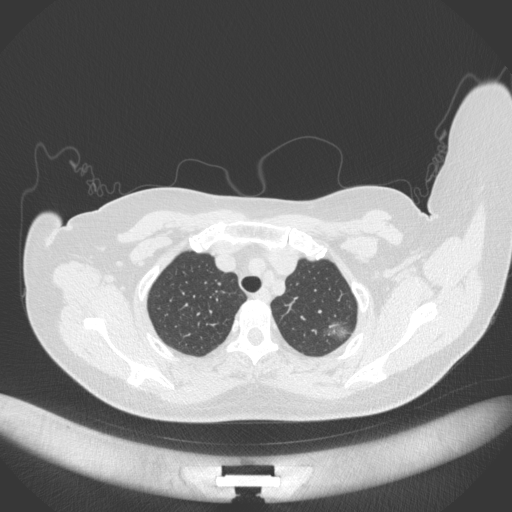
Chest CT, one axial slice. Position 311 of 386 along the scan axis. 120 kVp. Lung window (W 1500 / L -600 HU). 512 × 512 image matrix, field of view 400 × 400 mm. Patient: female, 58 years. Case-level facts recorded for this patient, not image findings: clinical TNM (as recorded): T1c N0 M0.
Structures marked on this image (rectangle marked by the reading radiologist):
- lung tumour (recorded histology: adenocarcinoma): box from (x=324, y=318) to (x=350, y=343) px